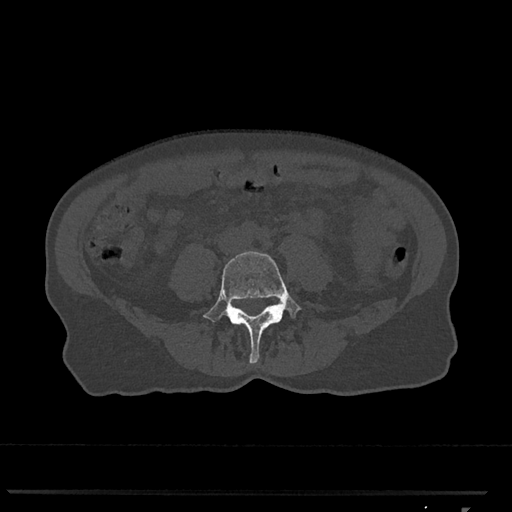
CT including the spine, one axial slice. Slice 209 of 793 in the series (ordered by position). Reconstruction kernel Br40s/3. Bone window (W 1800 / L 400 HU). 0.5 mm slice thickness. 512 × 512 image matrix. Female patient, age 62 years. From the clinical record (not read from this slice): primary cancer: renal.
Annotated regions visible in this slice (semi-automatic segmentation, software-assisted and operator-edited):
- L4 vertebra: bounding box (x1, y1, x2, y2) in pixels: (203, 251, 302, 364)